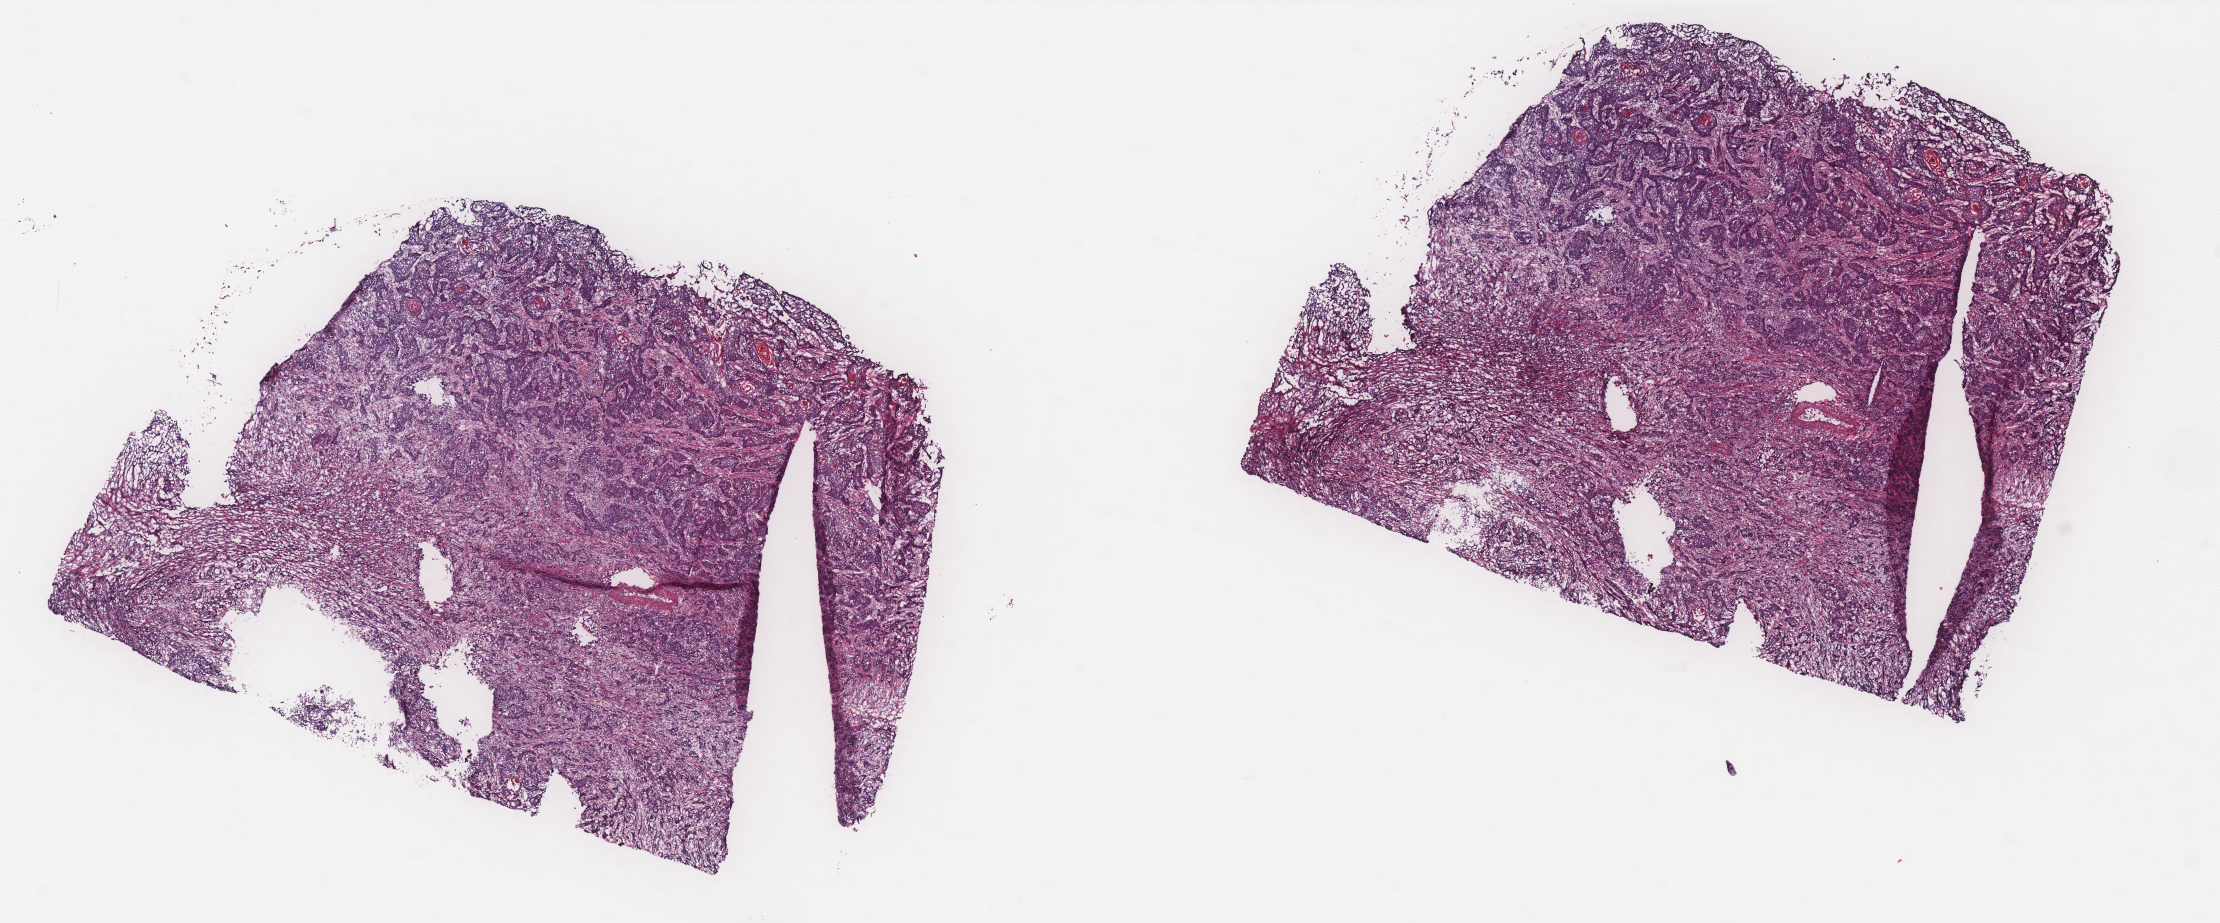
Hematoxylin and eosin (H&E) stained whole-slide image, shown as a low-resolution overview of the whole scanned area (about 17.8 x 7.4 mm, acquisition: 40x scan), frozen section from the top of the tissue portion, cervix, primary tumour sample. Patient: female, age at initial diagnosis 47 years. Histologic grade: G2 (moderately differentiated). Pathologist review of this section (percent, as recorded): tumour cells 80%, tumour nuclei 45%, normal cells 0%, stromal cells 20%, necrosis 0%. Infiltration values recorded for this section: lymphocyte infiltration 0%, monocyte infiltration 0%, neutrophil infiltration 0%.
Lymph nodes positive (case pathology): 0 of 19 examined. Histologic diagnosis: Squamous cell carcinoma, NOS.